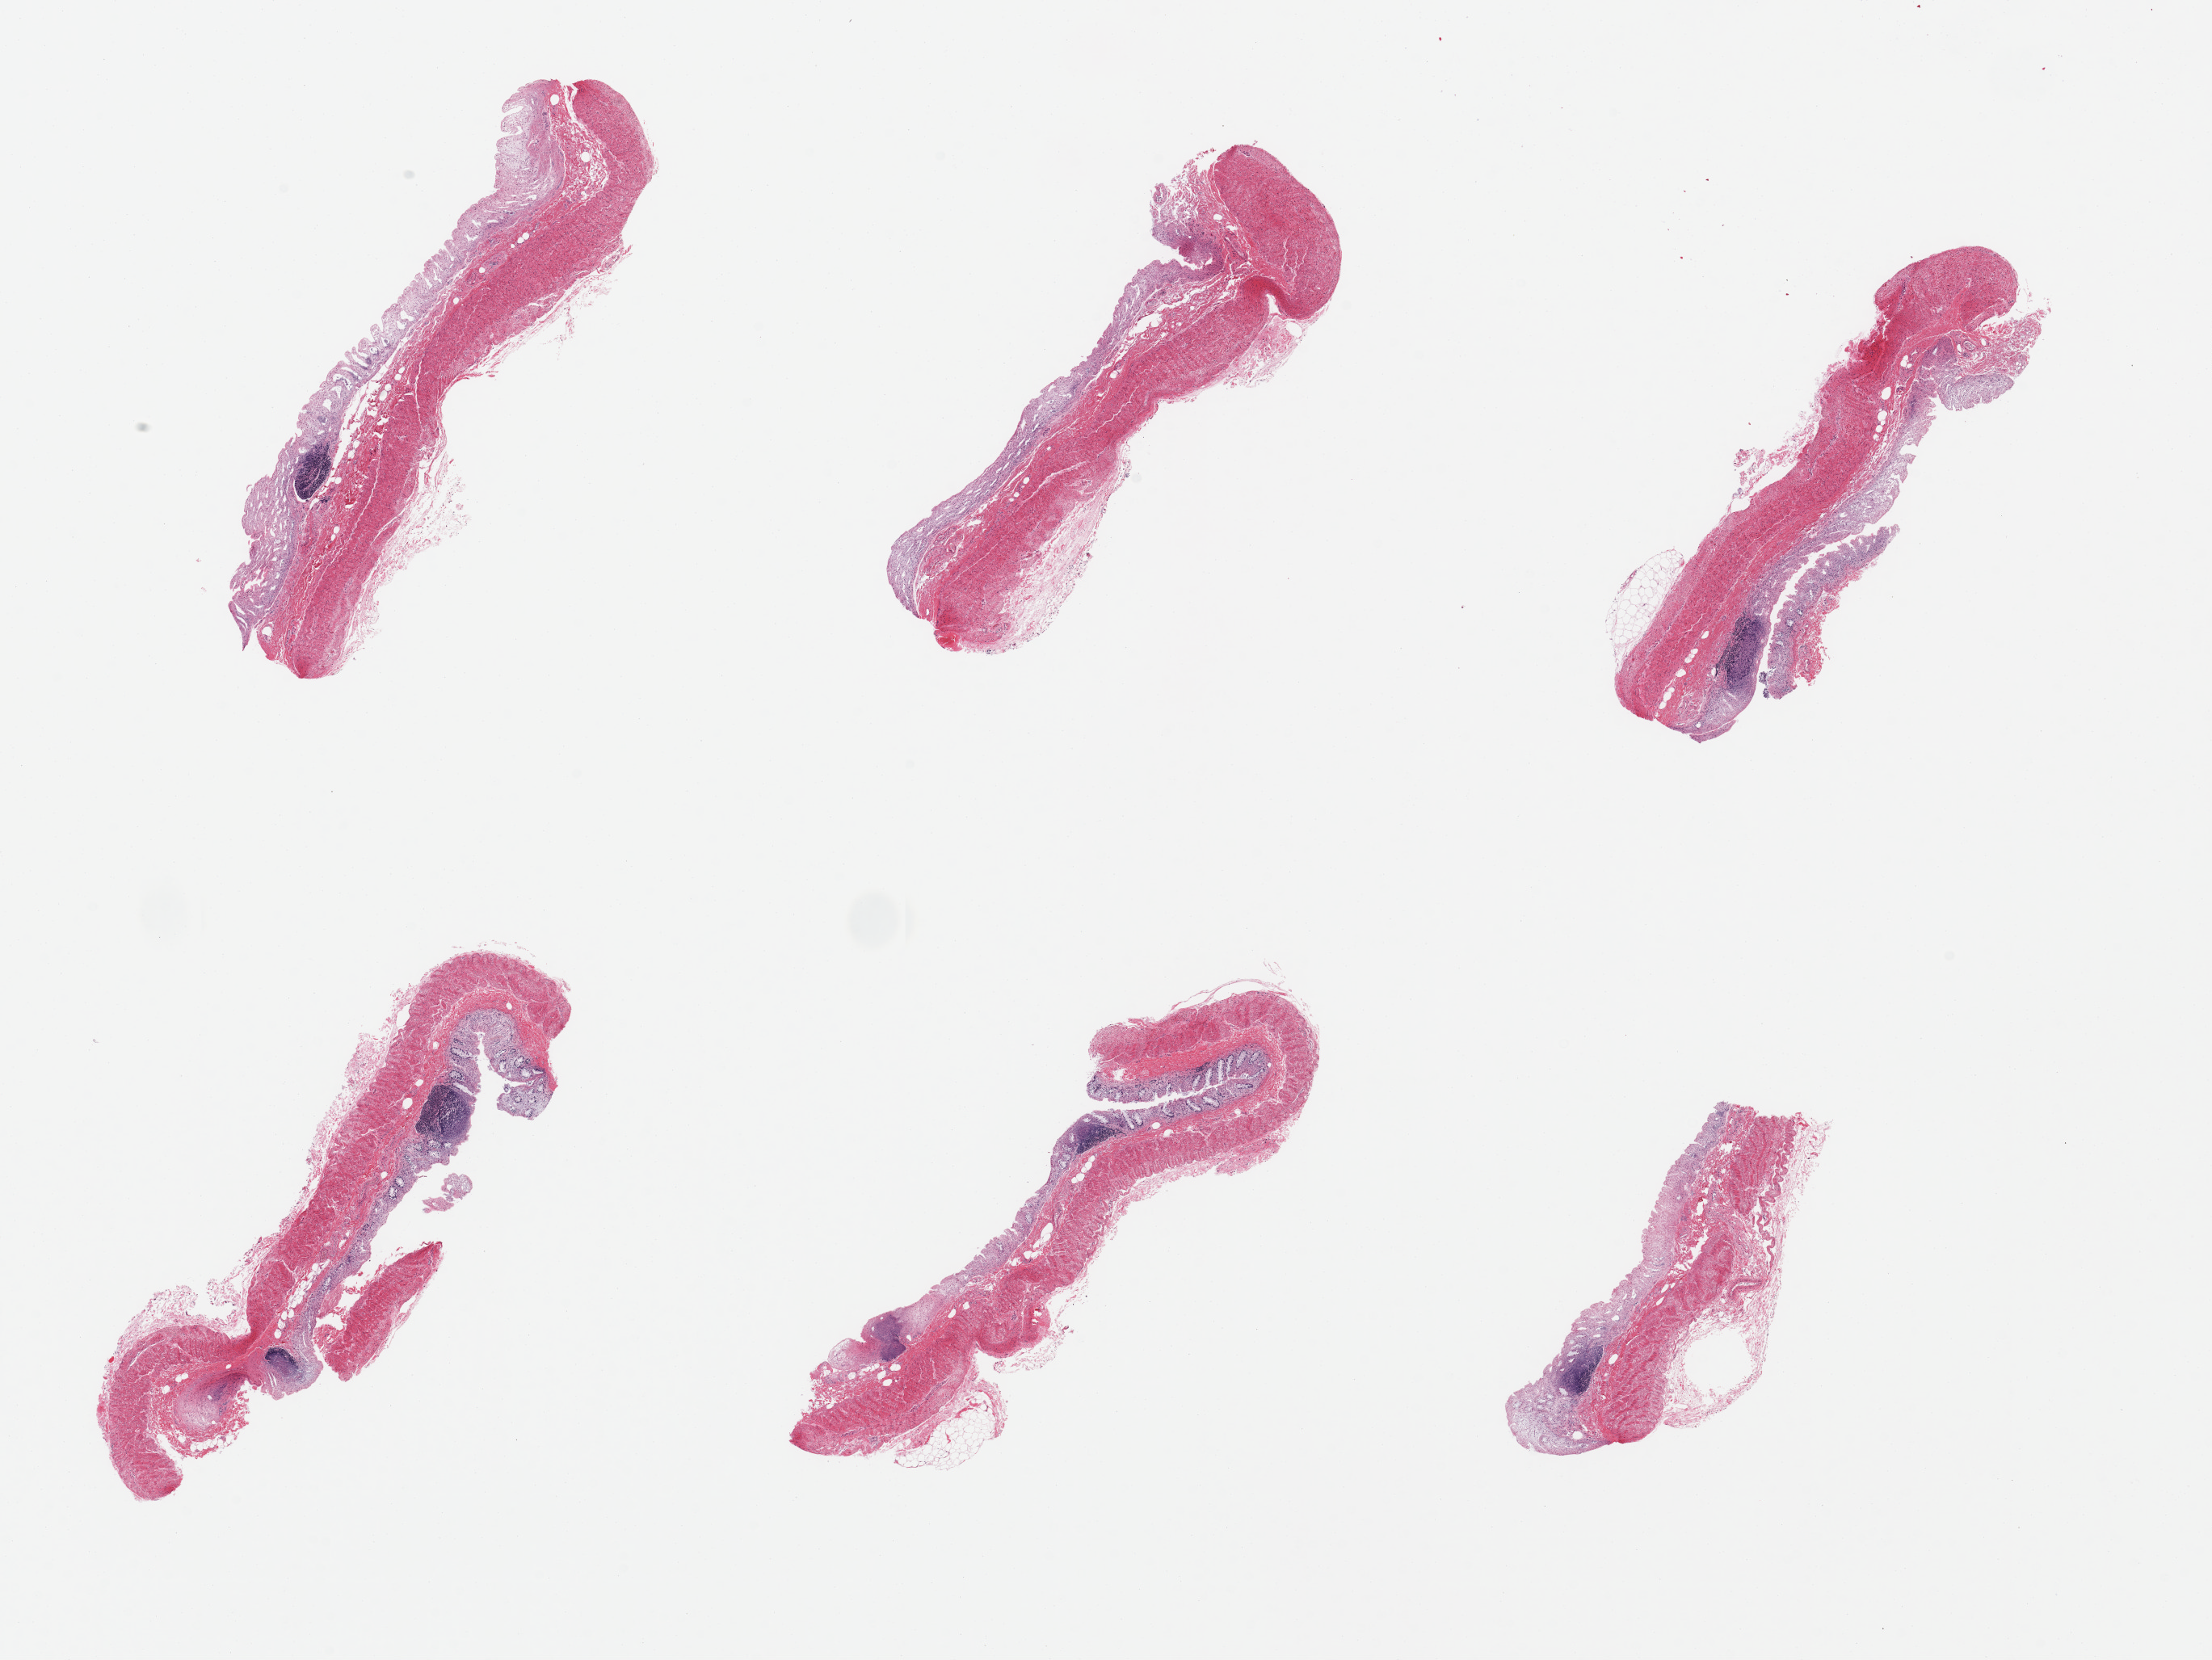
Whole-slide image, haematoxylin and eosin stain, a low-resolution overview of the entire scanned area, about 21.7 x 16.3 mm (acquisition: 20x scan), PAXgene-fixed, paraffin-embedded tissue, section of transverse colon (target tissue), donor tissue sample.
Reviewer comment on this tissue sample: 6 pieces, glandulare mucosa totally atuolyzed.